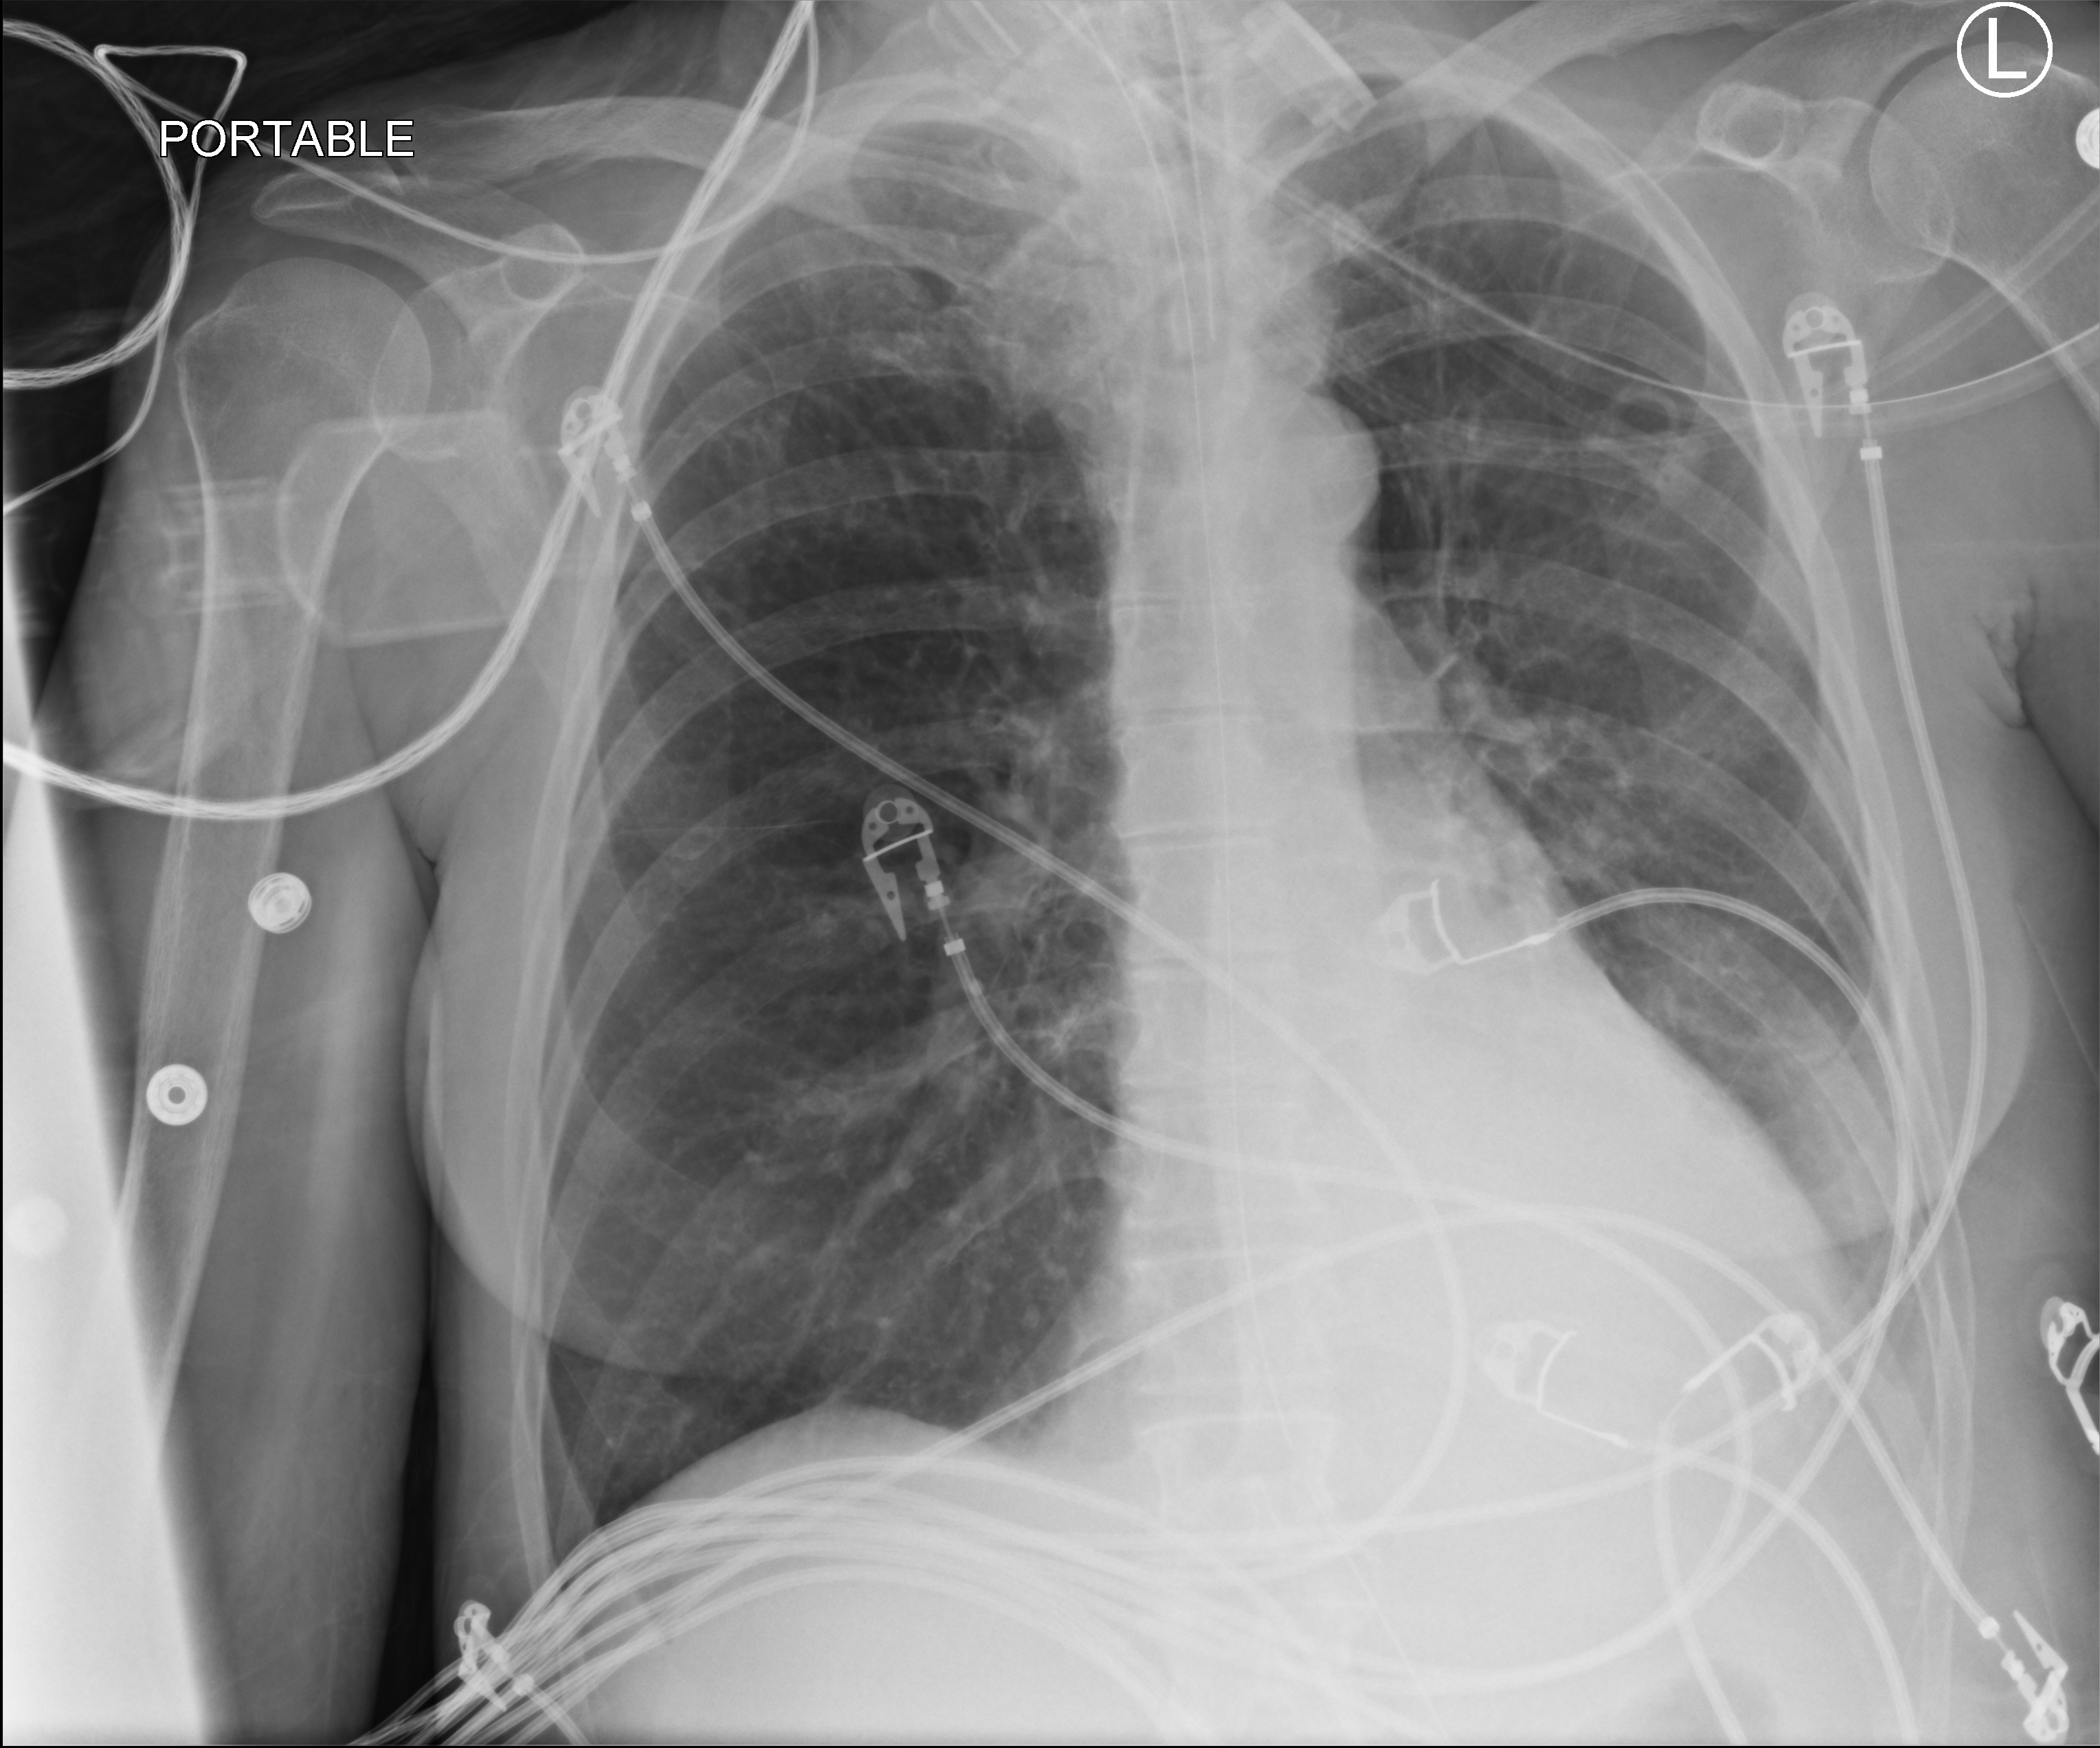
Bedside chest radiograph (computed radiography). Female patient hospitalised with COVID-19, age 60–74 years.
From the hospital-stay record, not from the radiograph (when in the stay this image was taken is not recorded): length of hospital stay: 38 days; mechanically ventilated during this hospital stay: yes; admitted to intensive care during this hospital stay: yes.